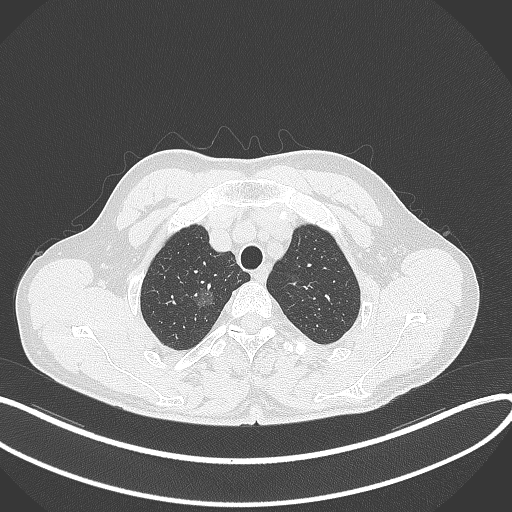
Chest CT, one axial slice. Position 322 of 407 along the scan axis. Reconstruction kernel B70f. 120 kVp. Lung window (W 1500 / L -600 HU). 1 mm slice thickness. 512 × 512 image matrix. Patient: male, 58 years. From the clinical record (not read from this slice): clinical TNM (as recorded): T1c N0 M0.
Annotated regions visible in this slice (rectangle marked by the reading radiologist):
- lung tumour (recorded histology: adenocarcinoma): bounding box [x1, y1, x2, y2] px = [184, 278, 221, 306]